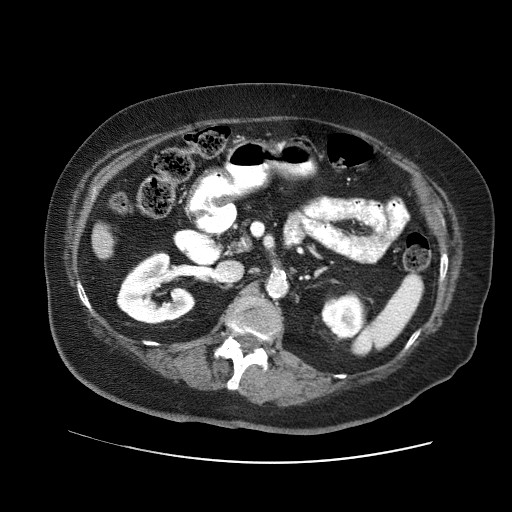
Contrast-enhanced abdominal CT (liver protocol), one axial slice; slice 10 of 71 in the series (ordered by position); soft-tissue window (W 400 / L 40 HU); 2.5 mm slice thickness; 512 × 512 image matrix, field of view 400 × 400 mm. Case-level facts recorded for this patient, not image findings: diagnosis: hepatocellular carcinoma (patient treated with transarterial chemoembolisation; whether this scan precedes or follows treatment is not stated here); TNM stage (as recorded): Stage-II; Child-Pugh class: A; tumour differentiation: poorly differentiated; tumour nodularity: multinodular.
Outlined on this slice (semi-automatically segmented with operator editing):
- liver parenchyma outside the tumour (the mass and vessels are separate outlines, so this box may not span the whole liver): bounding box <92,223,114,258> (left, top, right, bottom; pixels)